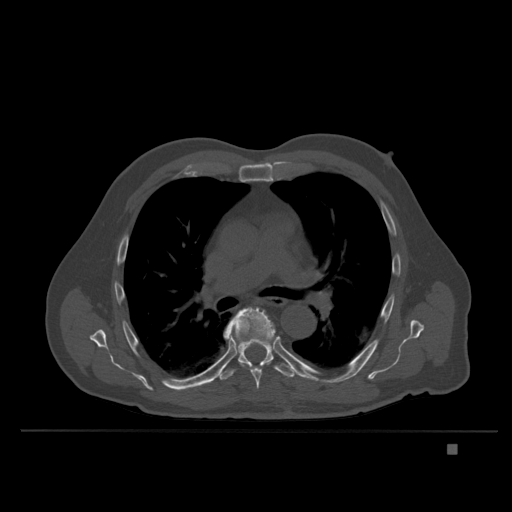
CT including the spine, one axial slice. Slice 252 of 435 in the series (ordered by position). Bone window (W 1800 / L 400 HU). 1.5 mm slice thickness. 512 × 512 image matrix, field of view 434 × 434 mm. Male patient, age 73 years. From the clinical record (not read from this slice): primary cancer: skin.
Outlined on this slice (semi-automatically segmented with operator editing):
- T6 vertebra: bounding box (x1, y1, x2, y2) in pixels: (223, 307, 276, 389)
- T7 vertebra: (209, 339, 299, 383)